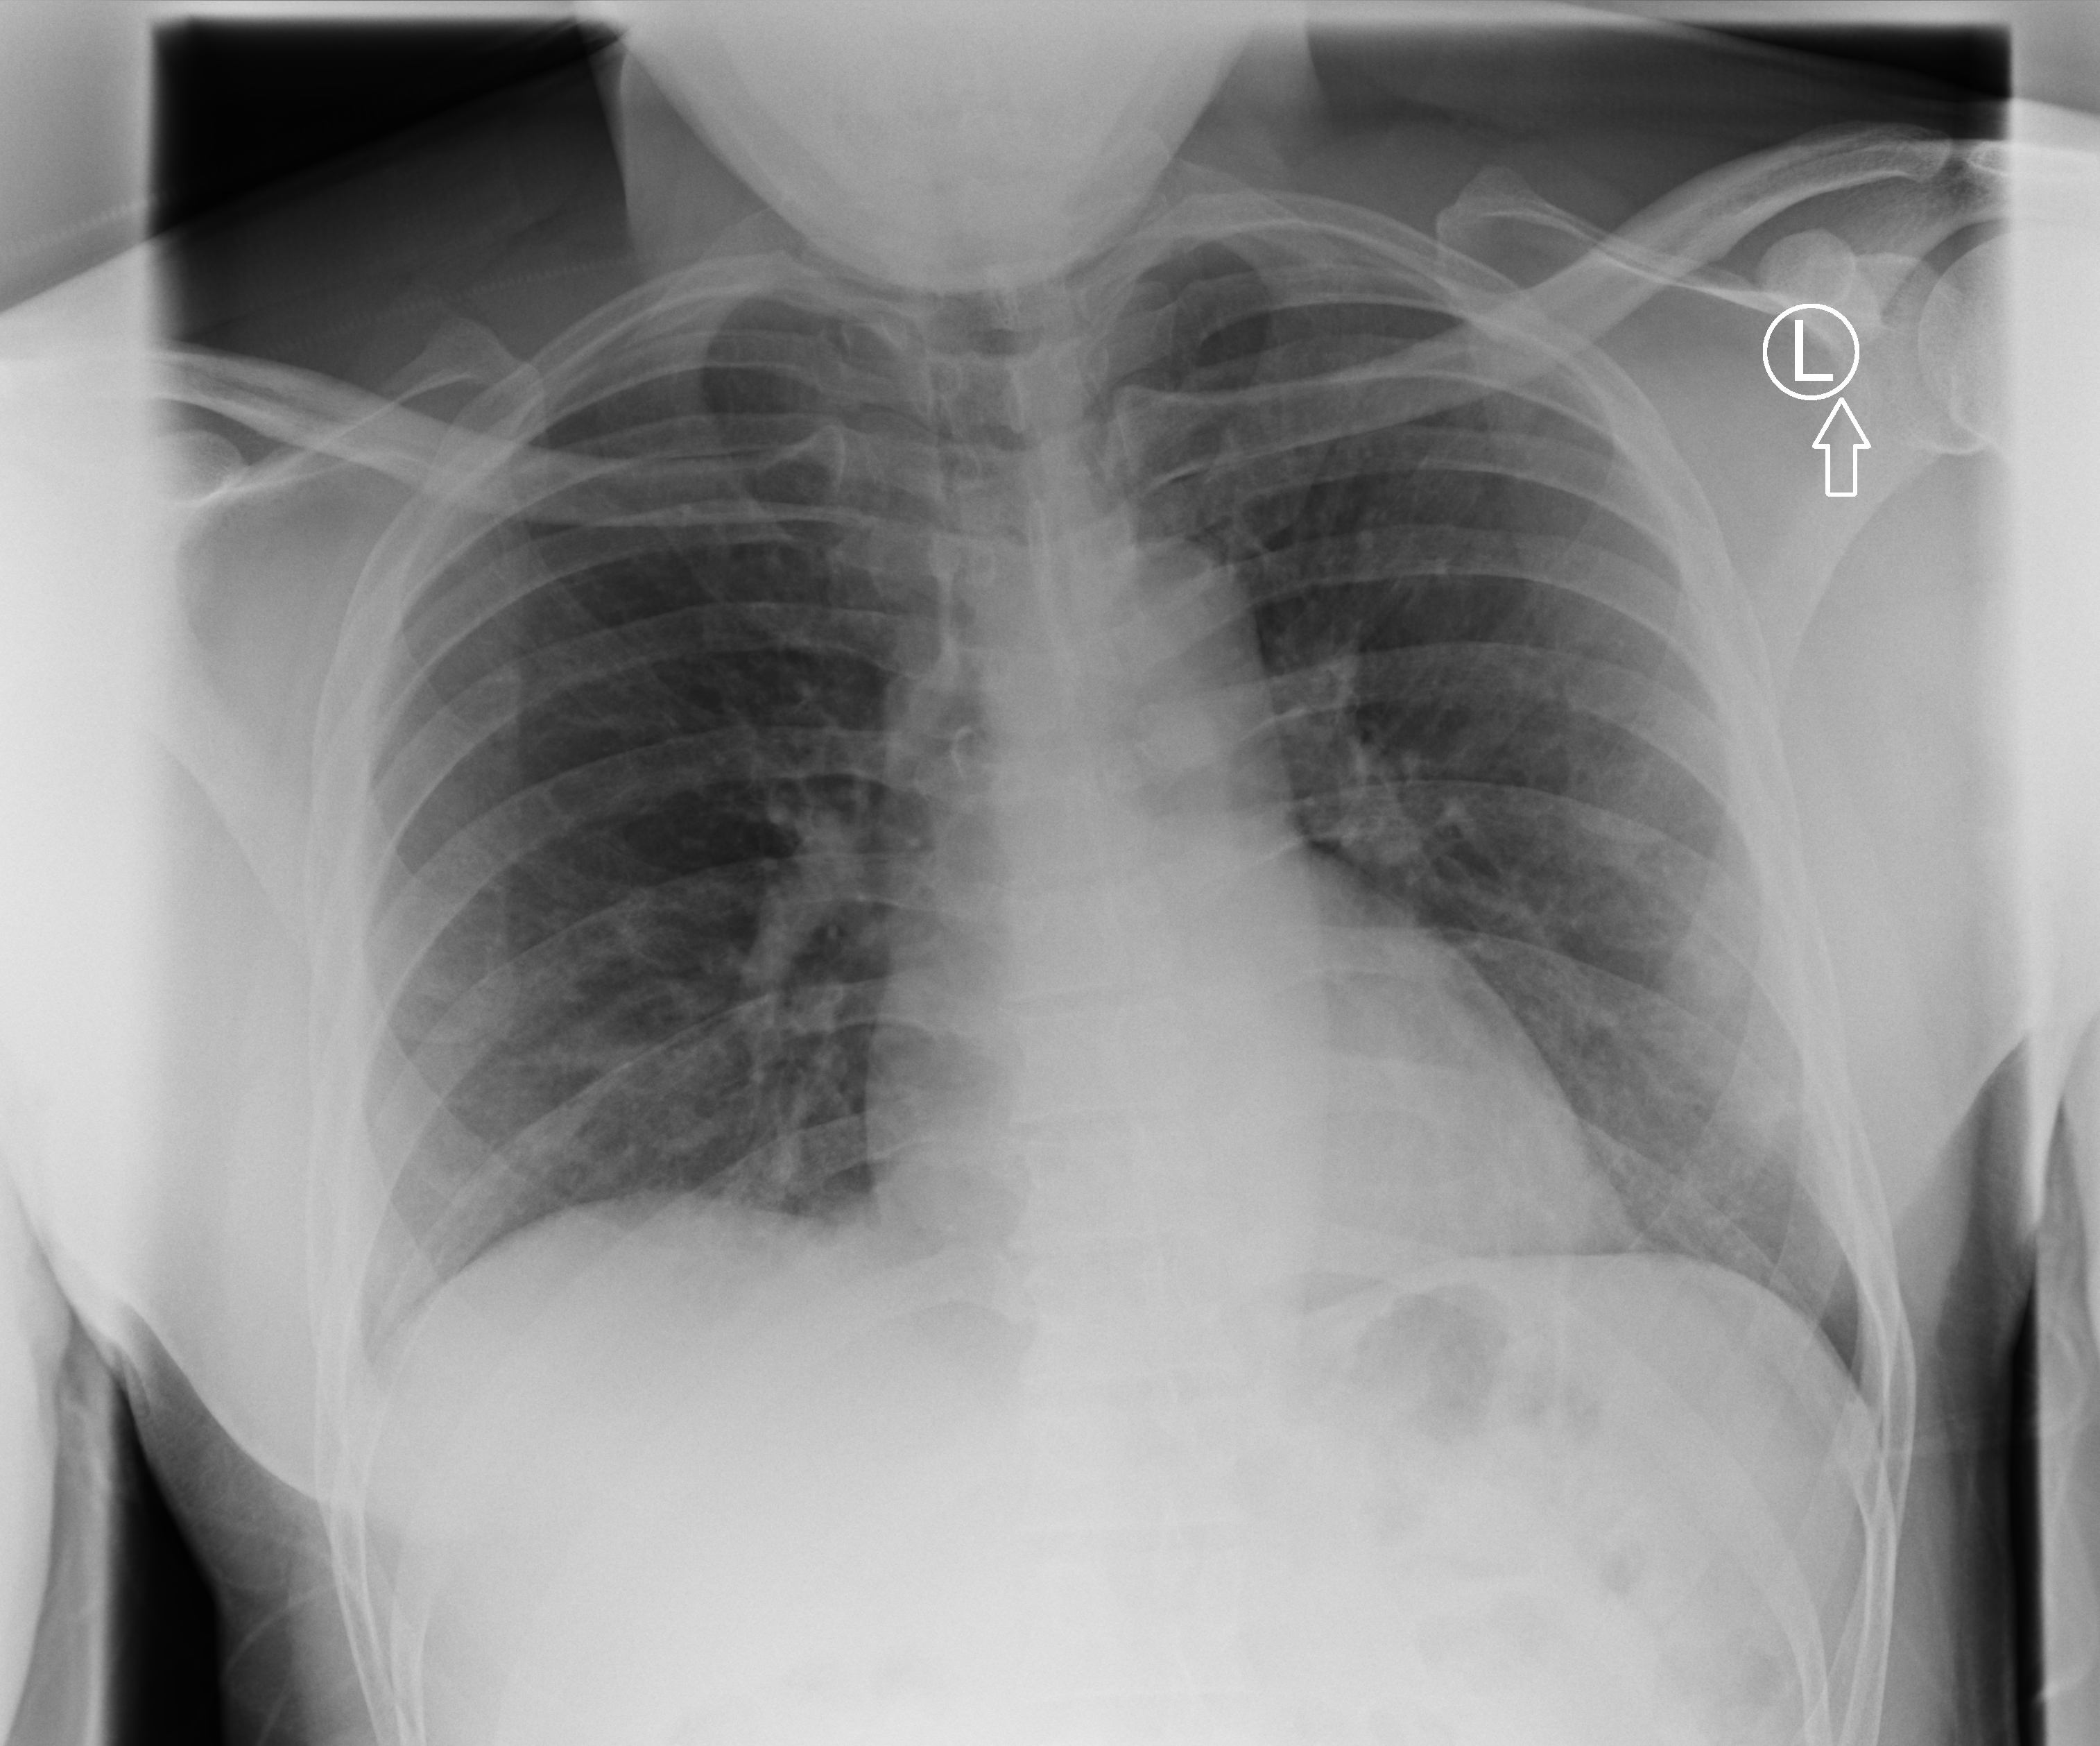
Bedside chest radiograph (computed radiography), anteroposterior (AP) projection. Male patient hospitalised with COVID-19, age 18–59 years.
Hospital-stay facts (about this admission, not read from this image; timing relative to this image not recorded): admitted to intensive care during this hospital stay: no; length of hospital stay: 2 days.